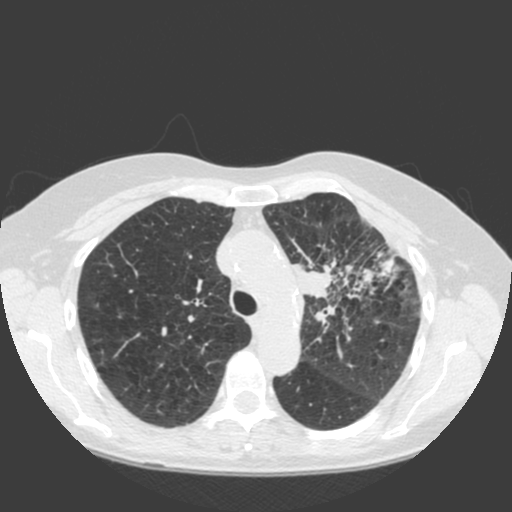
Low-dose screening chest CT, one axial slice; position 138 of 184 along the scan axis; 120 kVp; lung window (W 1500 / L -600 HU); 2 mm slice thickness; 512 × 512 image matrix, field of view 350 × 350 mm.
Outlined on this slice (expert manual segmentation):
- lesion 1 (tumor, hilum of left lung): bounding box [x1, y1, x2, y2] px = [292, 261, 338, 298]